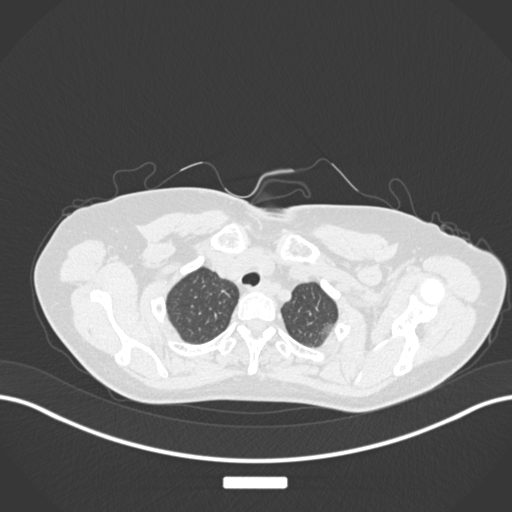
Chest CT, one axial slice; slice 155 of 181 in the series (ordered by position); reconstruction kernel B30f; 120 kVp; lung window (W 1500 / L -600 HU); 1 mm slice thickness; 512 × 512 image matrix. Female patient, age 58 years. Case-level facts recorded for this patient, not image findings: clinical TNM (as recorded): T1c N0 M0.
Outlined on this slice (rectangle marked by the reading radiologist):
- lung tumour (recorded histology: adenocarcinoma): bounding box [x1, y1, x2, y2] px = [314, 311, 340, 341]